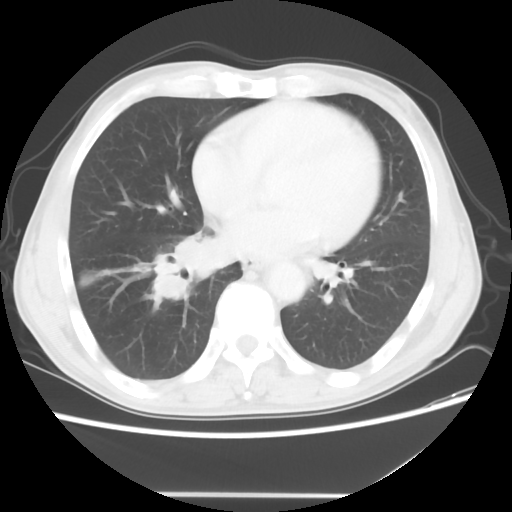
Chest CT, one axial slice. Position 22 of 56 along the scan axis. Reconstruction kernel STANDARD. 120 kVp. Lung window (W 1500 / L -600 HU). 5 mm slice thickness. 512 × 512 image matrix. Male patient, age 65 years. From the clinical record (not read from this slice): clinical TNM (as recorded): T1c N3 M0; histopathological grade: G3.
Annotated regions visible in this slice (rectangle marked by the reading radiologist):
- lung tumour (recorded histology: small cell carcinoma): box from (x=146, y=220) to (x=231, y=305) px